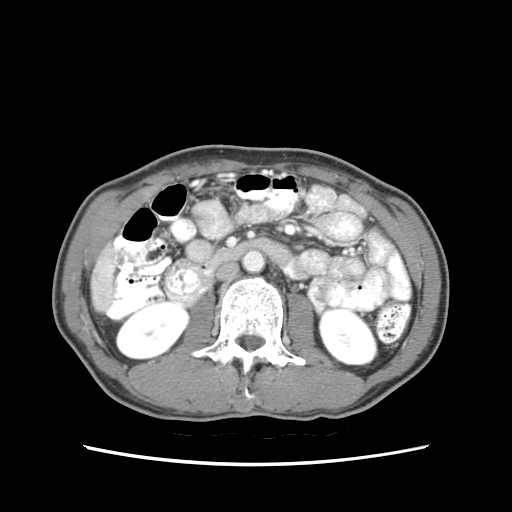
Contrast-enhanced abdominal CT (liver protocol), one axial slice. Position 11 of 79 along the scan axis. Soft-tissue window (W 400 / L 40 HU). 2.5 mm slice thickness. 512 × 512 image matrix, field of view 320 × 320 mm. From the clinical record (not read from this slice): diagnosis: hepatocellular carcinoma (patient treated with transarterial chemoembolisation; whether this scan precedes or follows treatment is not stated here); TNM stage (as recorded): Stage-IIIB.
Annotated regions visible in this slice (semi-automatically segmented with operator editing):
- liver parenchyma outside the tumour (the mass and vessels are separate outlines, so this box may not span the whole liver): box from (x=92, y=244) to (x=116, y=310) px
- liver vessels: (x=106, y=265)–(x=114, y=276)